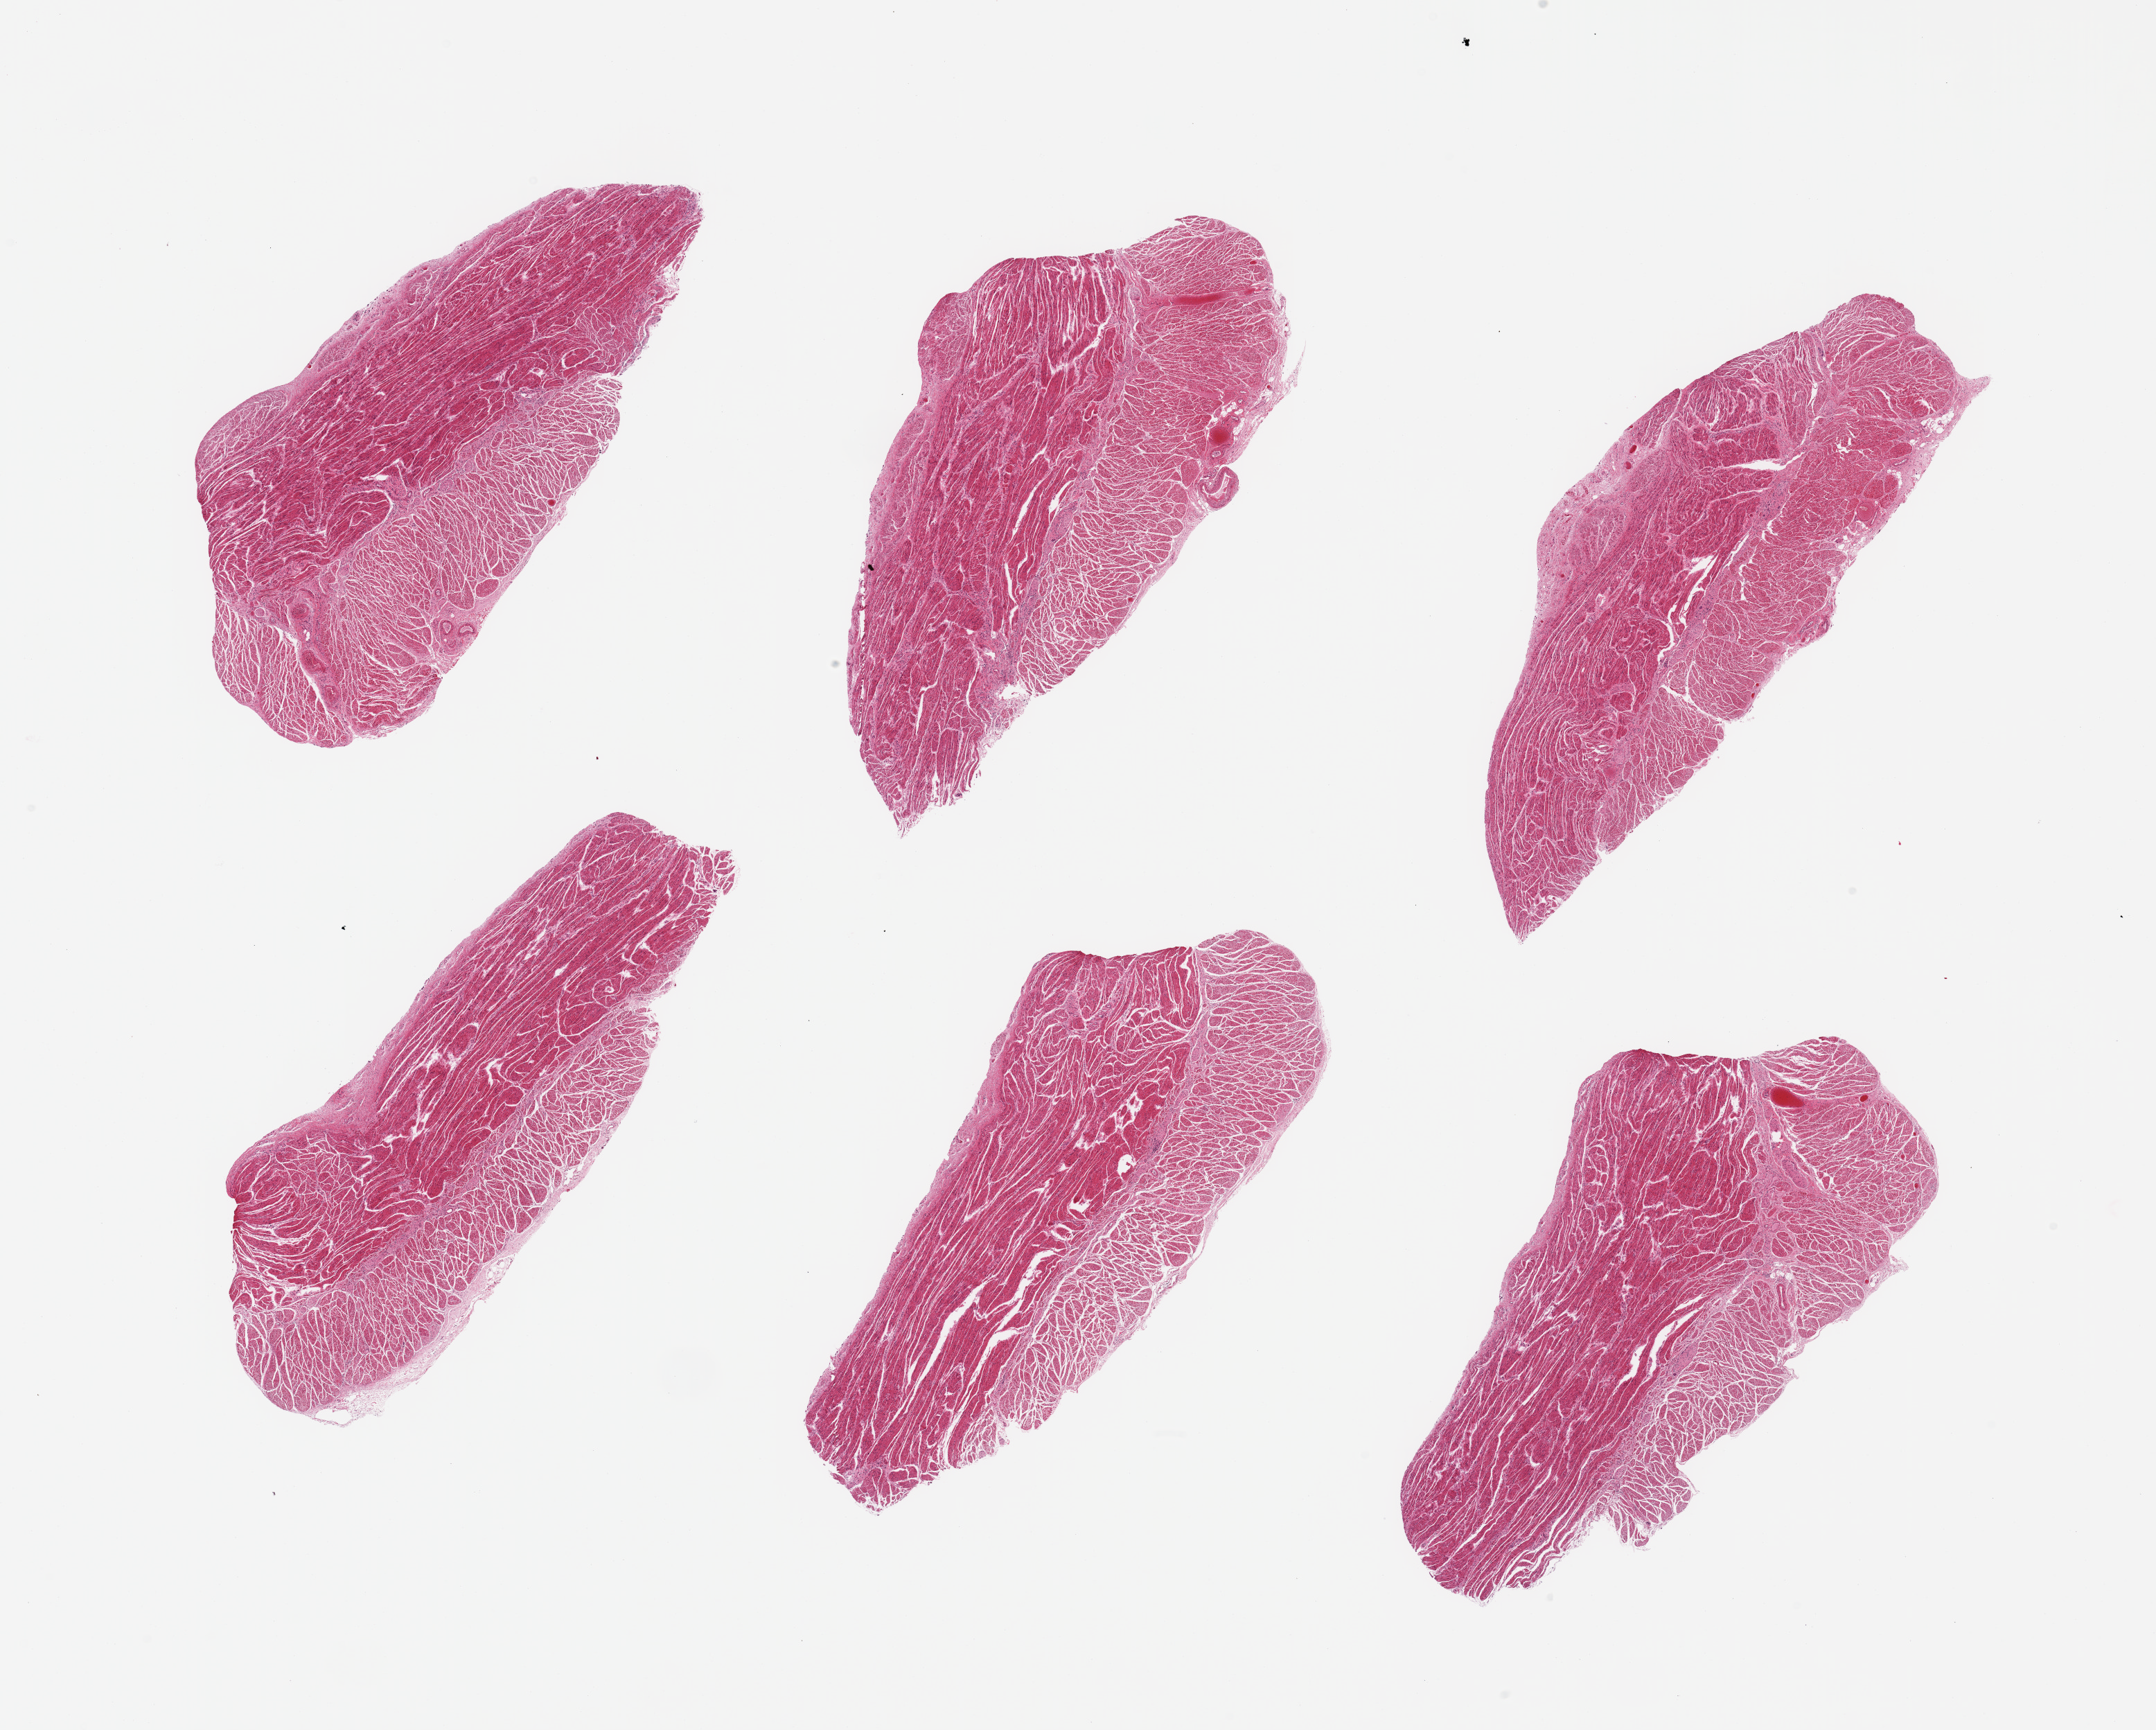
Whole-slide image, H&E stain, shown as a low-resolution overview of the whole scanned area (about 24.6 x 19.7 mm), PAXgene-fixed paraffin-embedded (PFPE) section, section of gastroesophageal junction (target tissue), donor tissue sample. Female donor.
• reviewer comment on this tissue sample: 6 pieces; well dissected